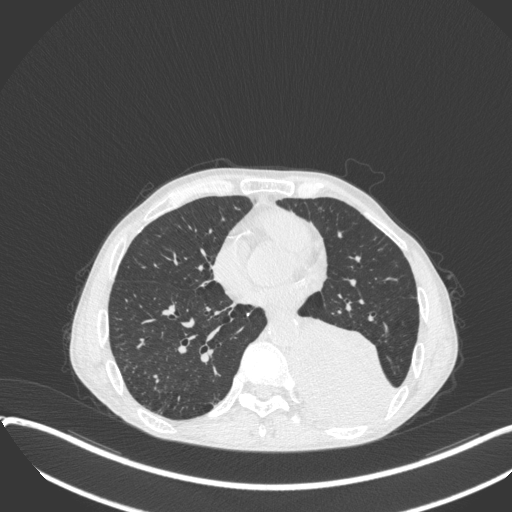
Chest CT, one axial slice; position 142 of 400 along the scan axis; reconstruction kernel B31f; lung window (W 1500 / L -600 HU); 1 mm slice thickness; 512 × 512 image matrix. Male patient, age 57 years. Case-level facts recorded for this patient, not image findings: clinical TNM (as recorded): T4 N0 M0.
Annotated regions visible in this slice (bounding box drawn by a radiologist):
- lung tumour (recorded histology: squamous cell carcinoma): box from (x=288, y=308) to (x=395, y=436) px